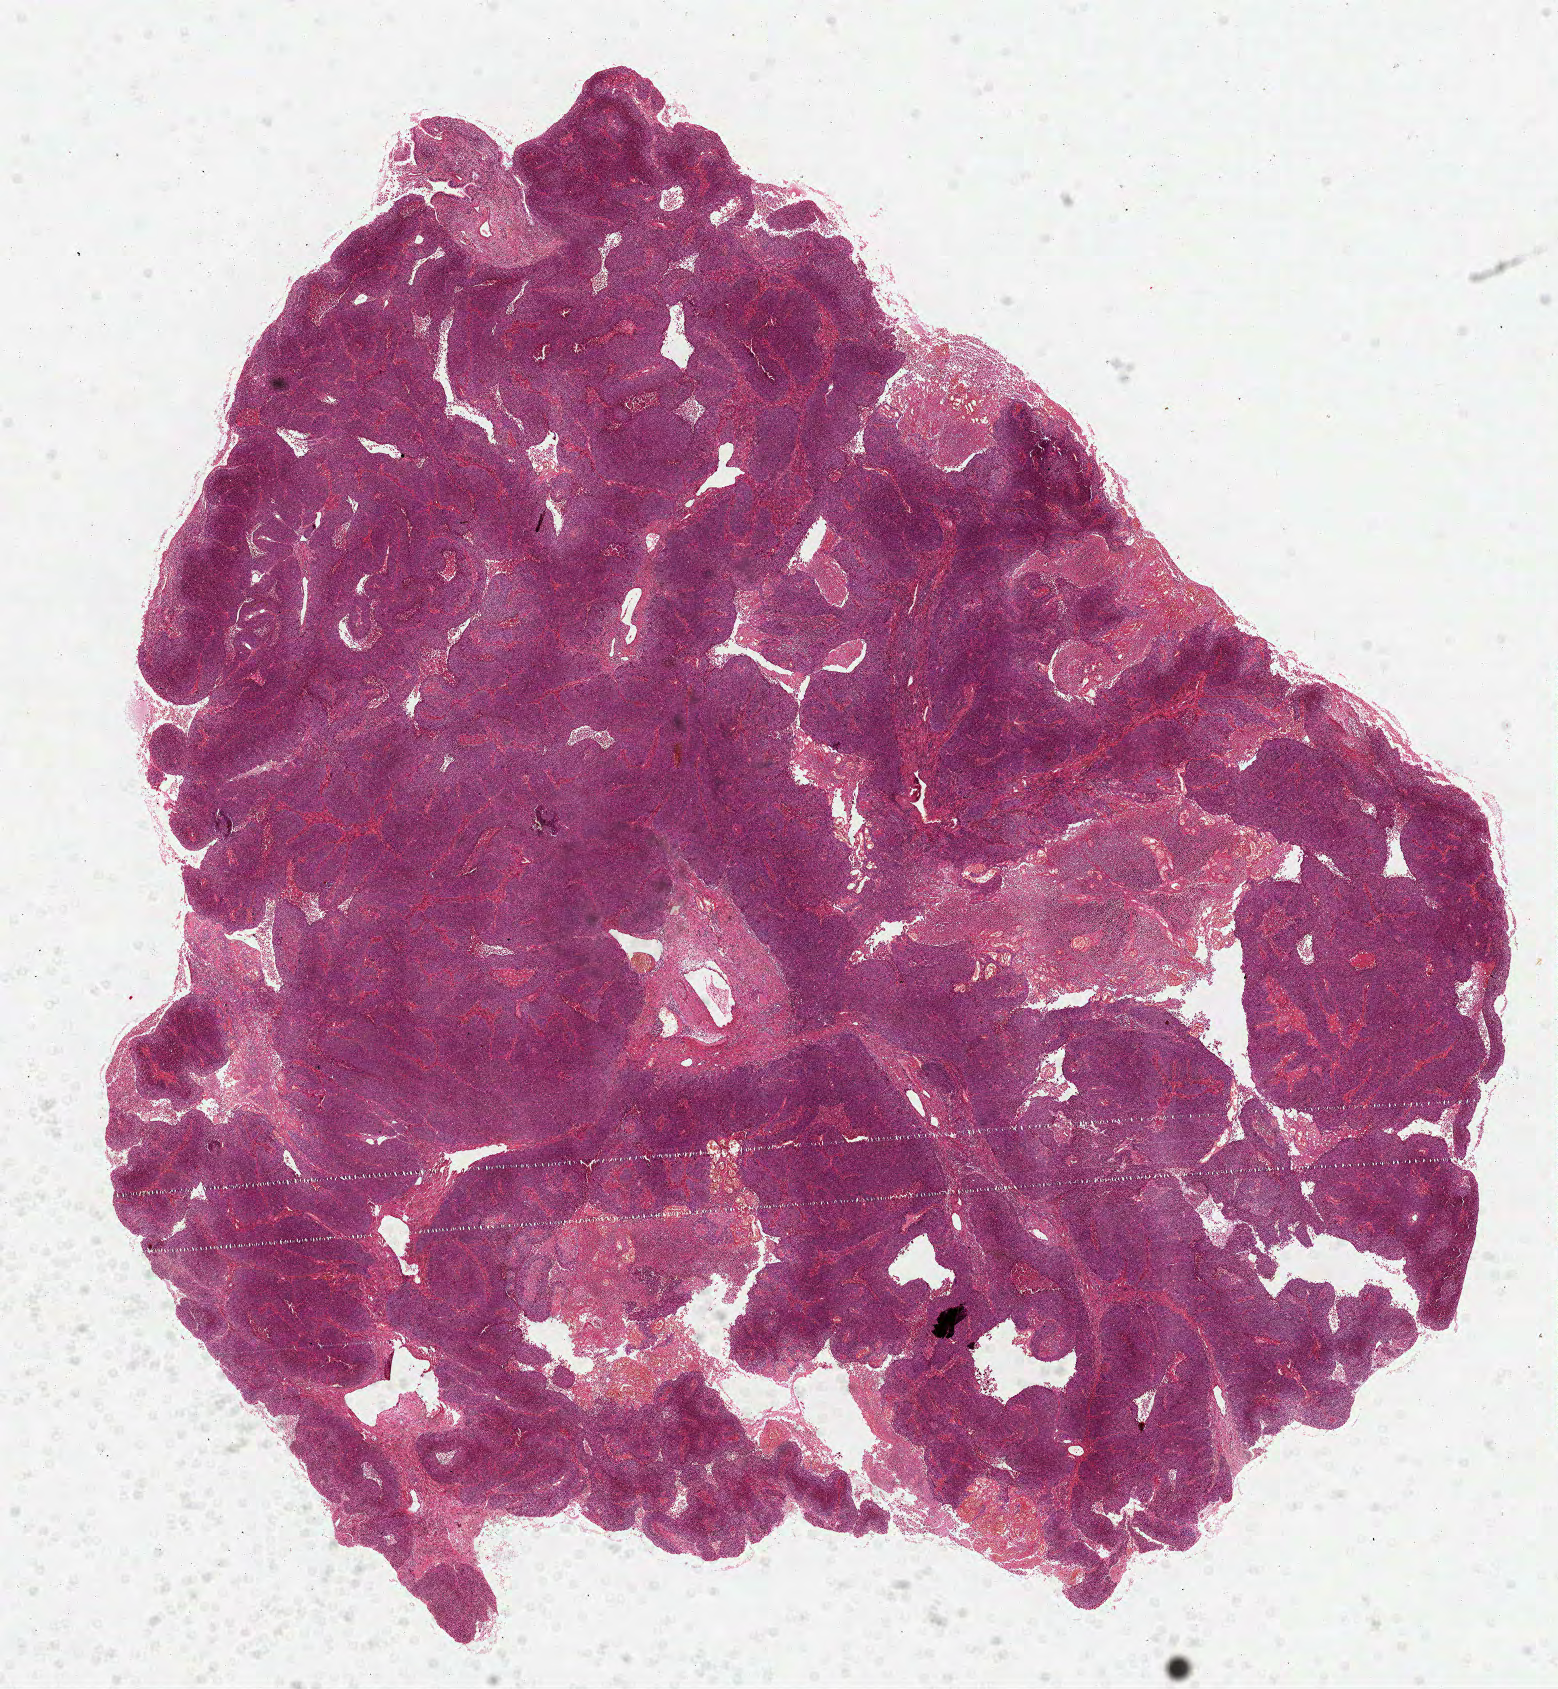
Digitized Hematoxylin and eosin (H&E) stained tissue section (whole slide) — a low-resolution overview of the entire scanned area, about 12.6 x 13.6 mm (slide scanned at 40x); FFPE section; lung, primary tumour sample. Male, age 65 years at initial diagnosis.
AJCC pathologic stage: IIA (6th edition). Pathologic diagnosis: Papillary squamous cell carcinoma (upper lobe, lung).